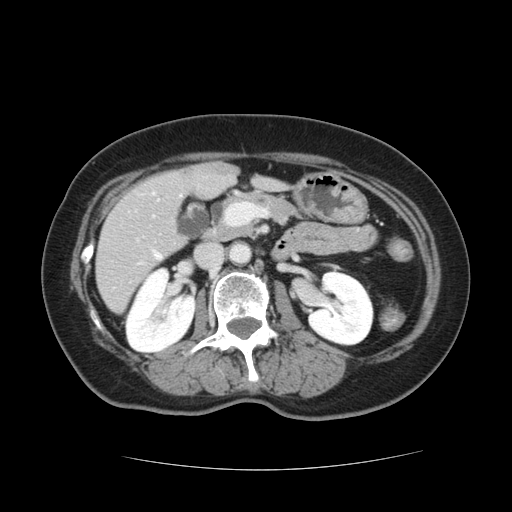
Contrast-enhanced abdominal CT, one axial slice. Position 49 of 128 along the scan axis. 120 kVp. Intravenous contrast given. Soft-tissue window (W 400 / L 40 HU). 512 × 512 image matrix. Female patient, age 67 years. Case-level facts recorded for this patient, not image findings: diagnosis: colorectal cancer liver metastases, imaged before liver resection; multiple liver metastases: yes; largest metastasis: 3 cm; disease in both lobes: yes.
Structures marked on this image (expert manual segmentation):
- hepatic veins: bounding box <154,252,162,259> (left, top, right, bottom; pixels)
- liver: <97,163,281,312>
- planned liver remnant (the part of the liver to remain after resection): <97,177,281,312>
- portal vein (with intrahepatic branches): <139,216,155,264>